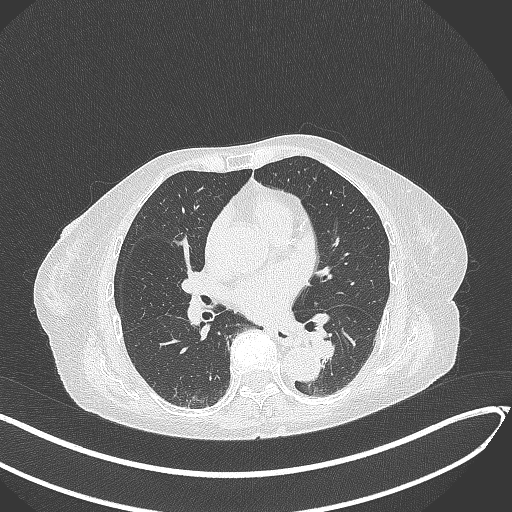
Chest CT, one axial slice; 120 kVp; lung window (W 1500 / L -600 HU); 1 mm slice thickness; 512 × 512 image matrix, field of view 400 × 400 mm. Female patient, age 82 years. Case-level facts recorded for this patient, not image findings: clinical TNM (as recorded): T1b N0 M1.
Annotated regions visible in this slice (bounding box drawn by a radiologist):
- lung tumour (recorded histology: adenocarcinoma): bounding box <305,332,344,367> (left, top, right, bottom; pixels)